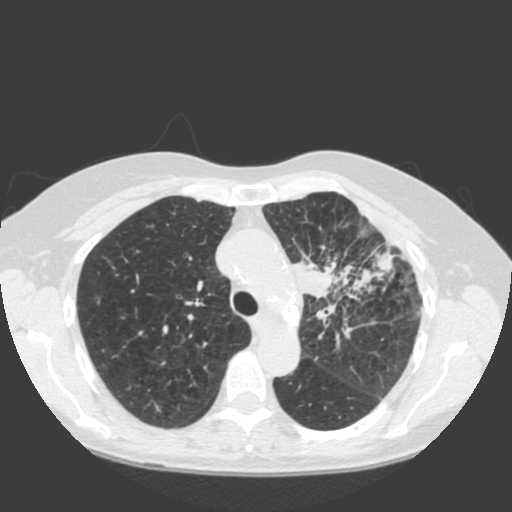
Chest CT (low-dose screening protocol), one axial image; first (baseline) screen; lung window (W 1500 / L -600 HU); 2 mm slice thickness; 120 kVp; slice 48 of 184 in the series. Female, age 66 years at enrolment. Current smoker at enrolment.
Expert reader's lesion annotation, bounding box [x1, y1, x2, y2] px = [285, 240, 397, 340]. Reader record for this screening exam (exam-level; its link to the box is not recorded): non-calcified nodule or mass ≥4 mm, left upper lobe, 61 × 45 mm, spiculated (stellate) margins, soft tissue attenuation.